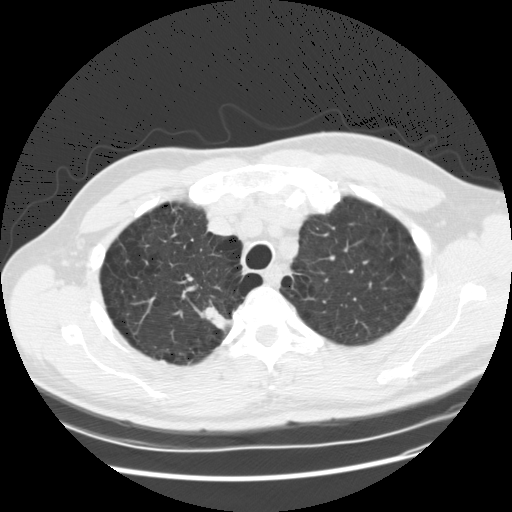
Axial slice from a low-dose chest CT screening exam, baseline annual screen, lung window (W 1500 / L -600 HU), standard (soft-tissue) reconstruction kernel (STANDARD), slice 27 of 132 in the series. Male, age 61 years at enrolment. Former smoker at enrolment.
Lesion marked by an expert reader, bounding box <191,289,239,340> (left, top, right, bottom; pixels). Reader record for this screening exam (exam-level; its link to the box is not recorded): non-calcified nodule or mass ≥4 mm, right upper lobe, 19 × 13 mm, poorly defined margins, soft tissue attenuation. Participant outcome: lung cancer diagnosed 62 days after this screen — squamous cell carcinoma, NOS, right upper lobe, poorly differentiated (G3), stage IA (AJCC 6th edition), 20 mm at pathology.